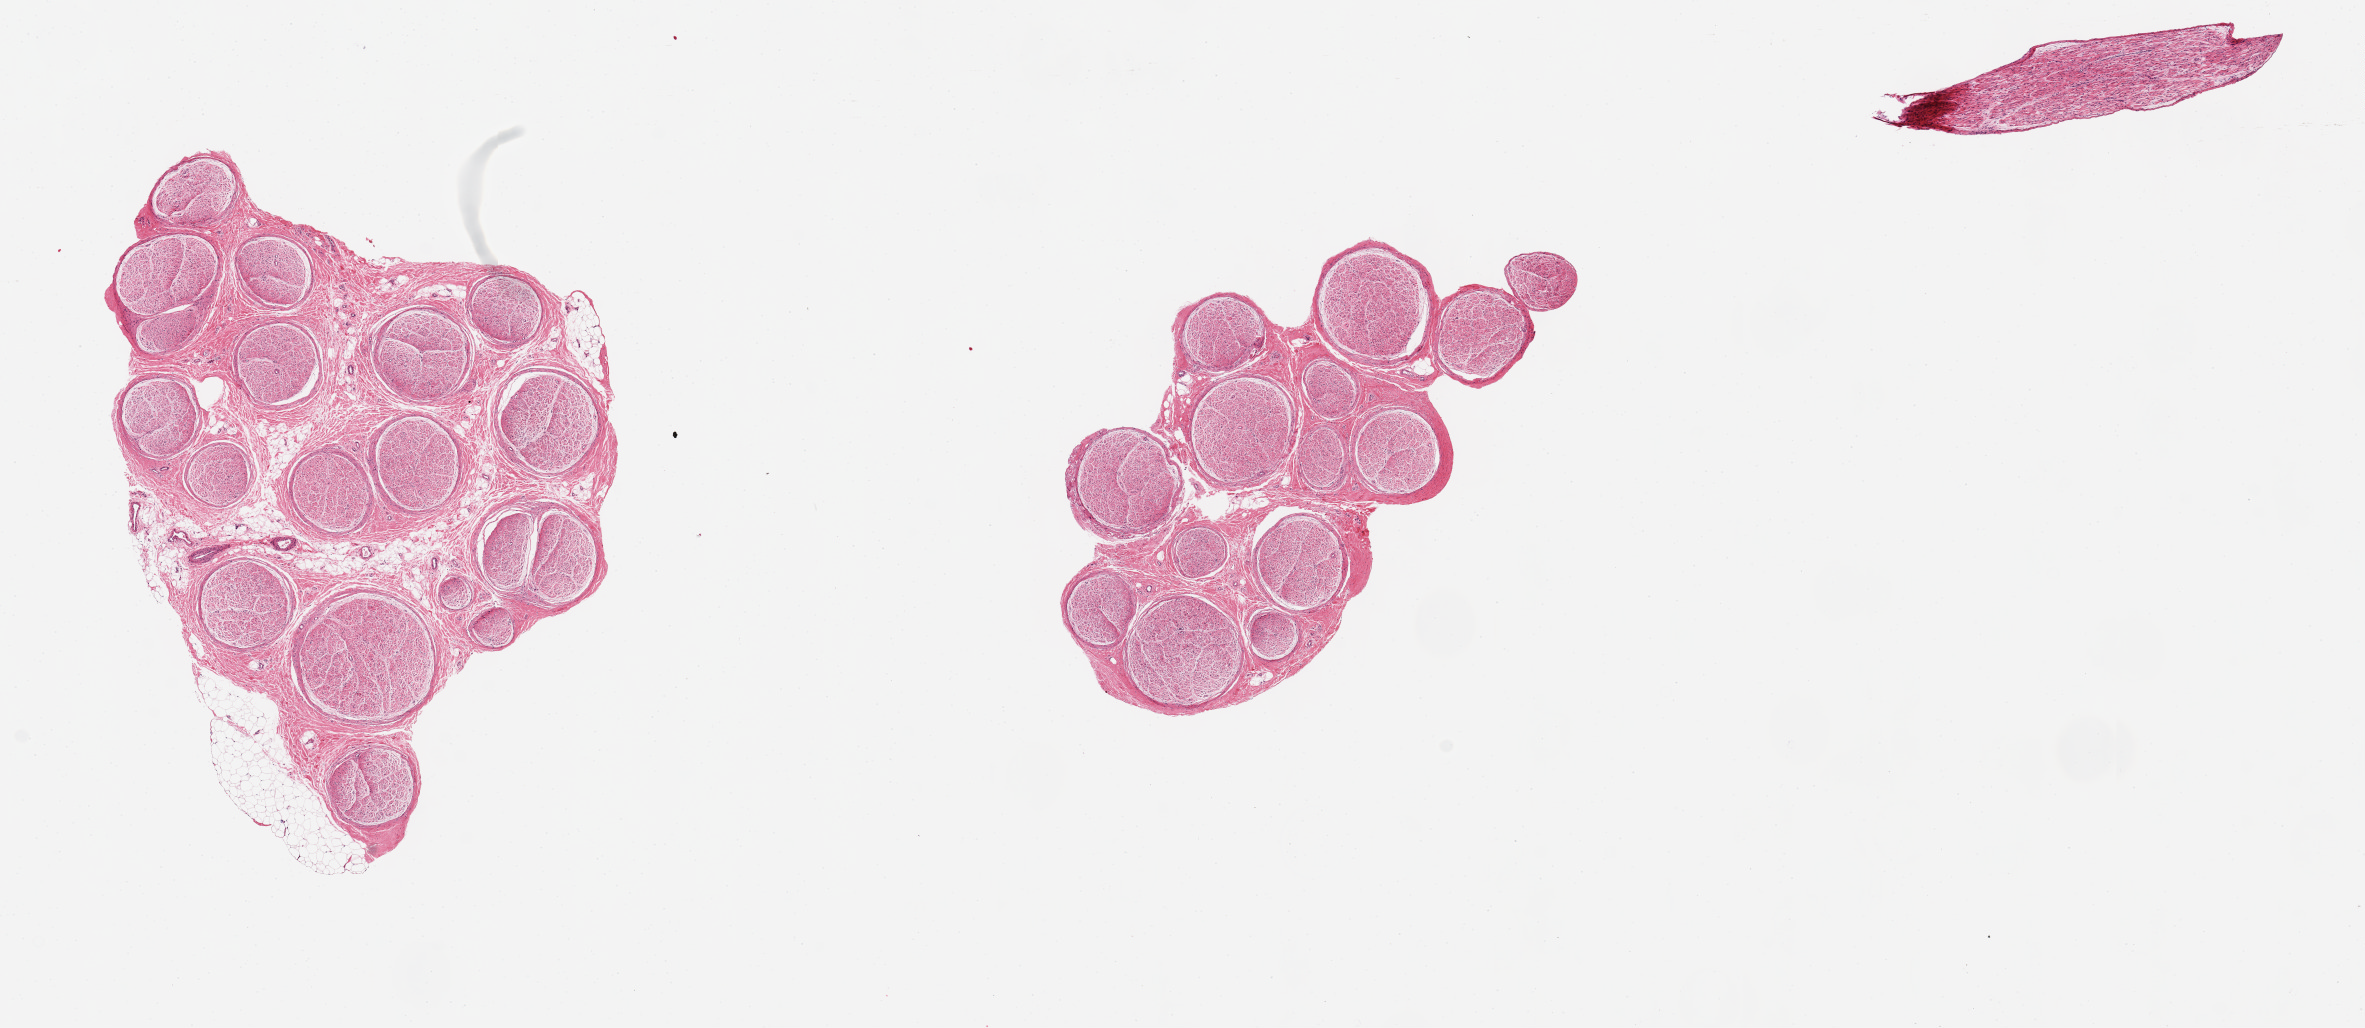
Whole-slide image, haematoxylin and eosin stain, shown as a low-resolution overview of the whole scanned area (about 18.7 x 8.1 mm). PAXgene-fixed paraffin-embedded (PFPE) section. Sampled site (target tissue): tibial nerve. Donor tissue sample. Donor: female.
Review note (as recorded): 2 ~ 5.5x3.5mm aliquots, clean specimens.